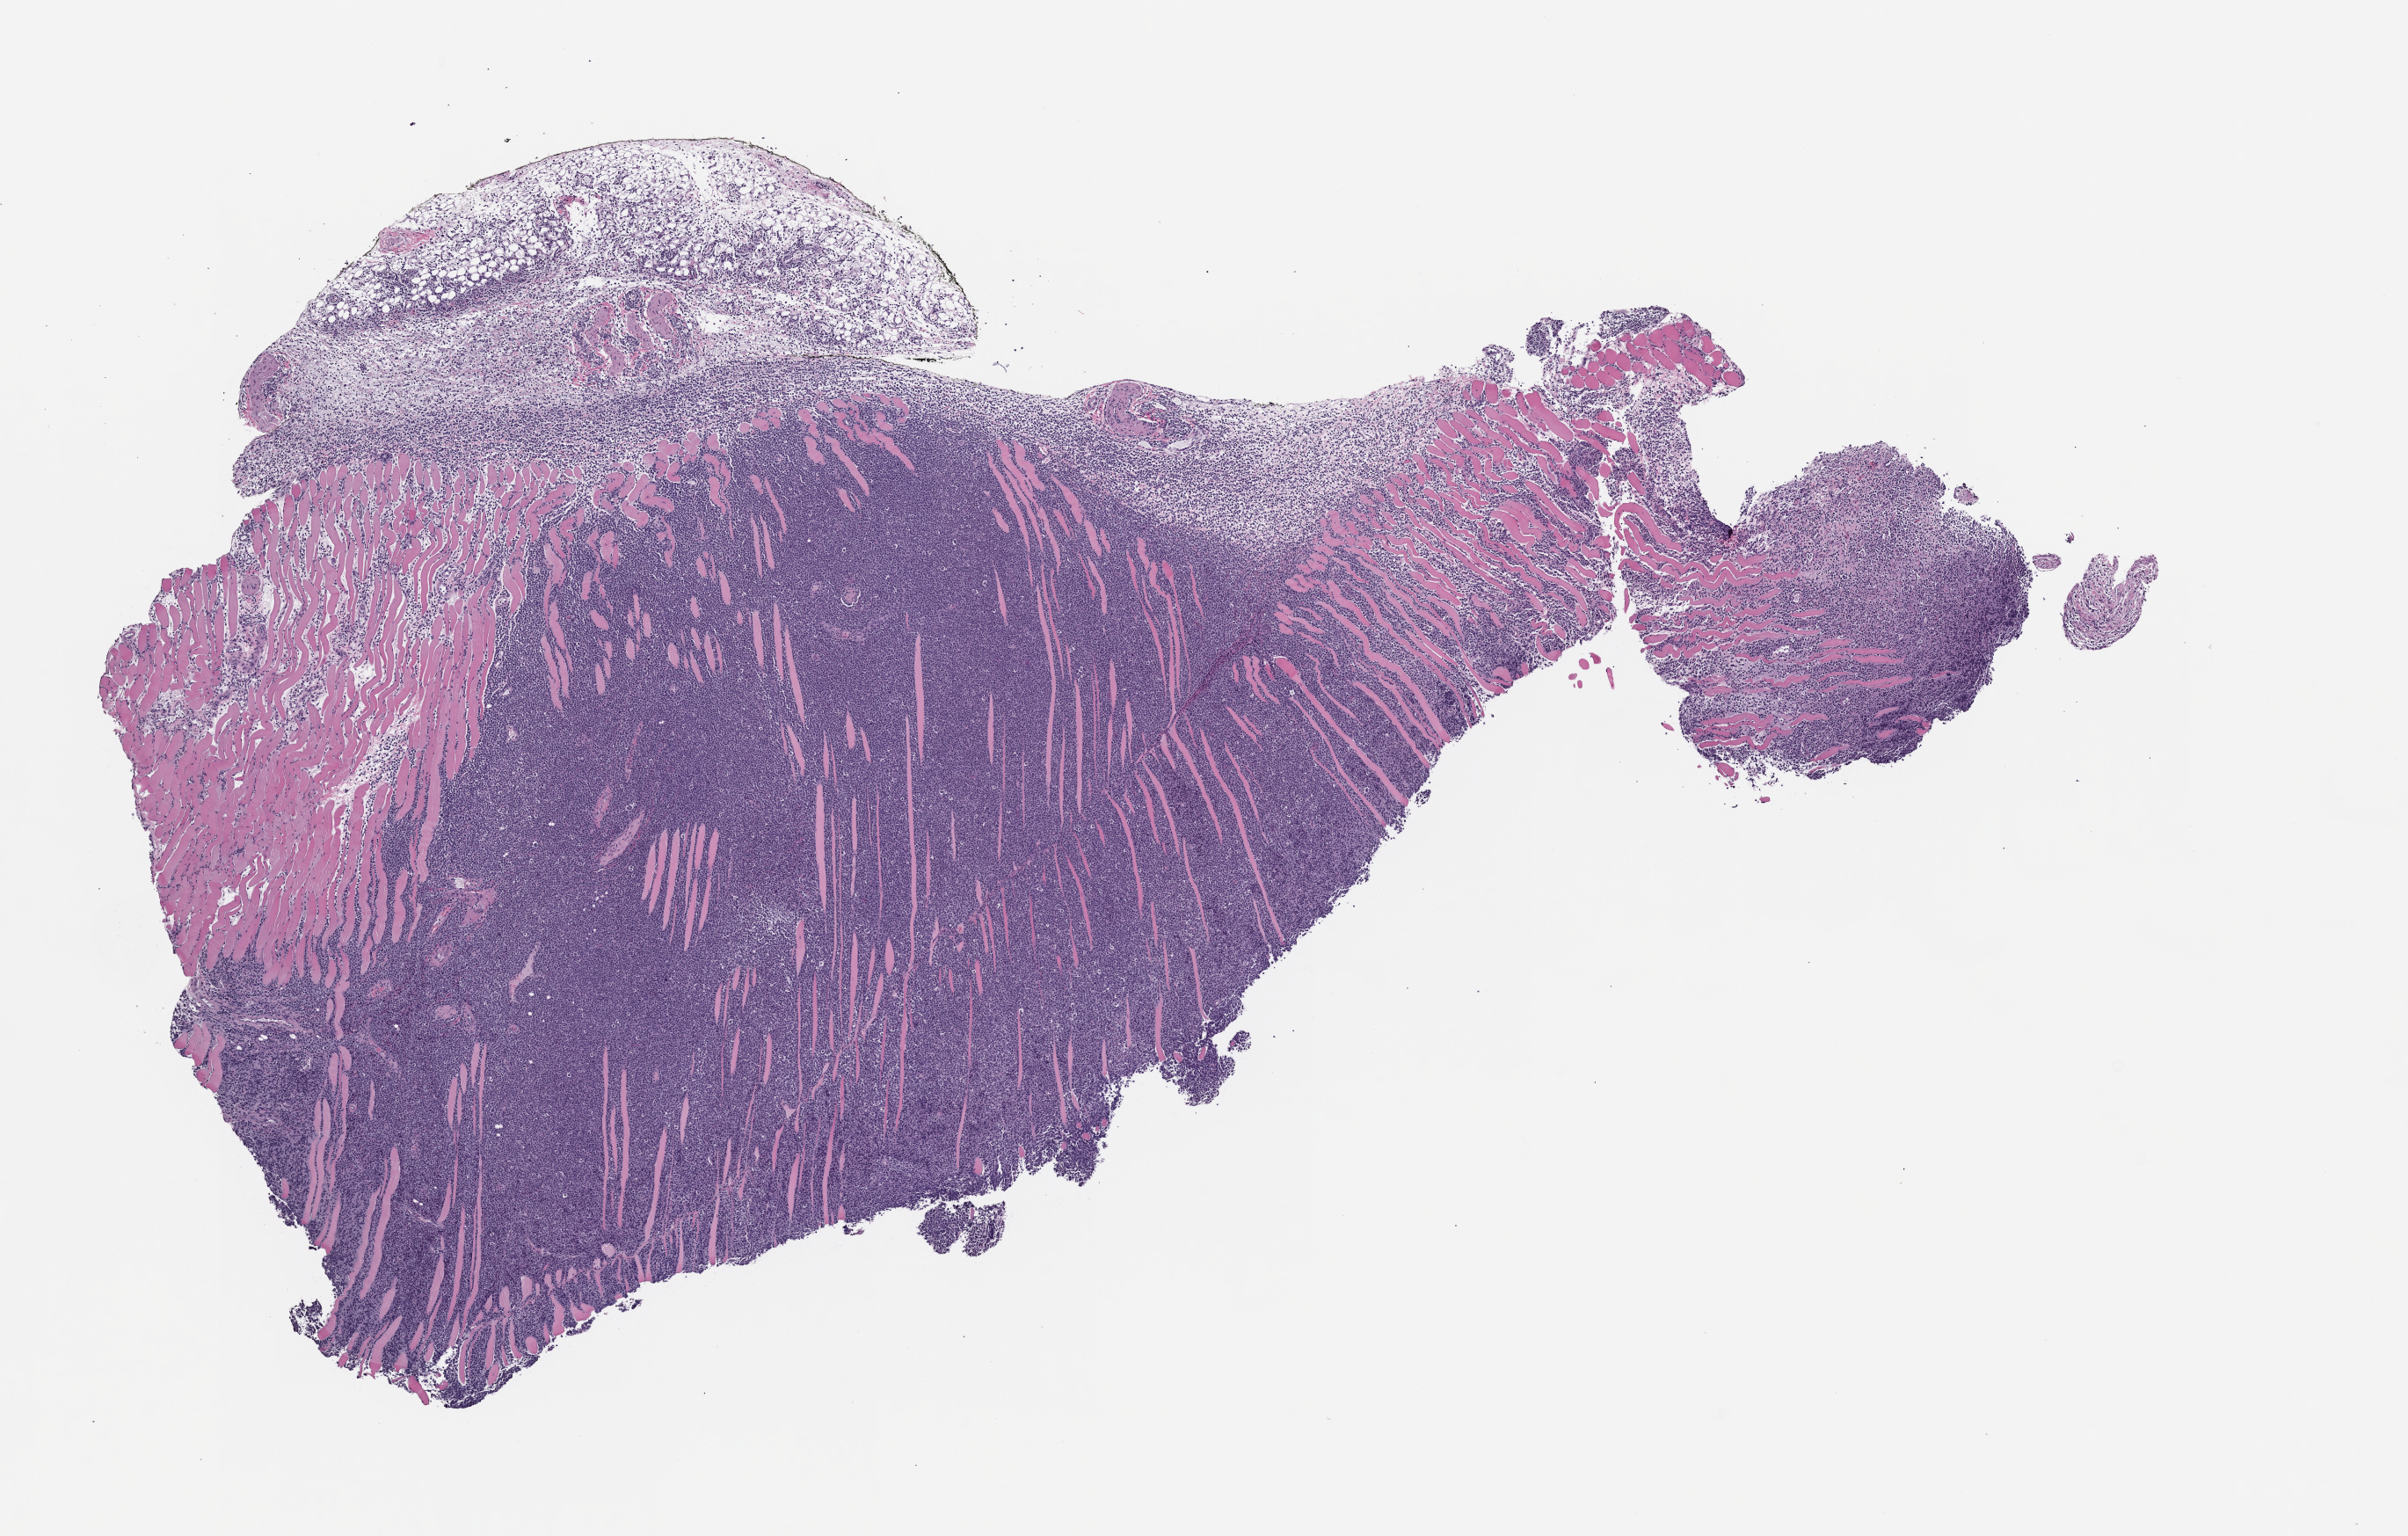
Whole-slide image, H&E: patient-derived xenograft (human tumor grown in a mouse) — a low-resolution overview of the entire scanned area, about 11.0 x 7.0 mm.
Specimen: FFPE section.